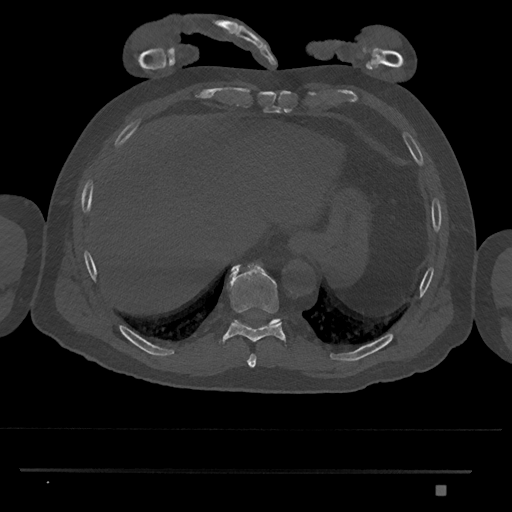
CT including the spine, one axial slice. Position 1049 of 1134 along the scan axis. Reconstruction kernel Br40s/3. 120 kVp. Bone window (W 1800 / L 400 HU). 0.5 mm slice thickness. 512 × 512 image matrix, field of view 429 × 429 mm. Male patient, age 65 years. Case-level facts recorded for this patient, not image findings: primary cancer: prostate.
Structures marked on this image (semi-automatic segmentation, software-assisted and operator-edited):
- T10 vertebra: box from (x=234, y=318) to (x=281, y=324) px
- T8 vertebra: (x=247, y=354)–(x=256, y=367)
- T9 vertebra: (x=220, y=264)–(x=285, y=343)